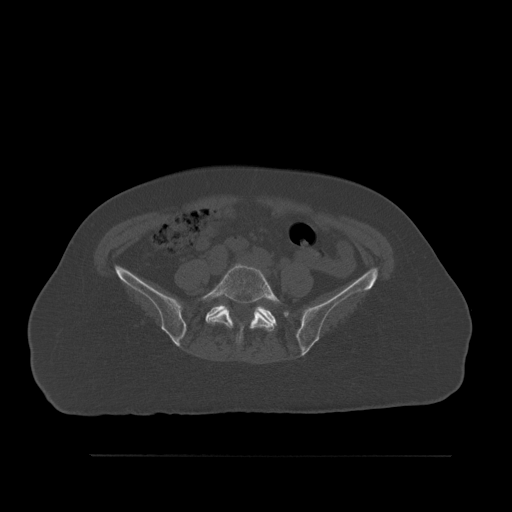
CT including the spine, one axial slice. Position 186 of 527 along the scan axis. Bone window (W 1800 / L 400 HU). 1.5 mm slice thickness. 512 × 512 image matrix, field of view 470 × 470 mm. Patient: female, 73 years. Case-level facts recorded for this patient, not image findings: primary cancer: breast.
Structures marked on this image (semi-automatic segmentation, software-assisted and operator-edited):
- L5 vertebra: bounding box [x1, y1, x2, y2] px = [199, 263, 282, 345]